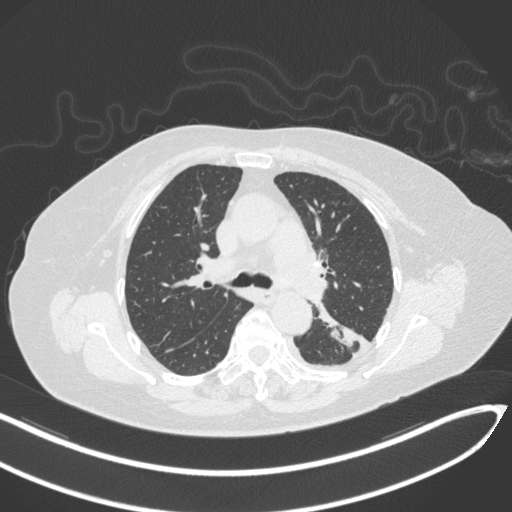
Chest CT, one axial slice; position 204 of 270 along the scan axis; 120 kVp; lung window (W 1500 / L -600 HU); 512 × 512 image matrix, field of view 400 × 400 mm. Female patient, age 76 years. From the clinical record (not read from this slice): clinical TNM (as recorded): T1c N0 M0.
Structures marked on this image (bounding box drawn by a radiologist):
- lung tumour (recorded histology: adenocarcinoma): bounding box <312,301,360,347> (left, top, right, bottom; pixels)